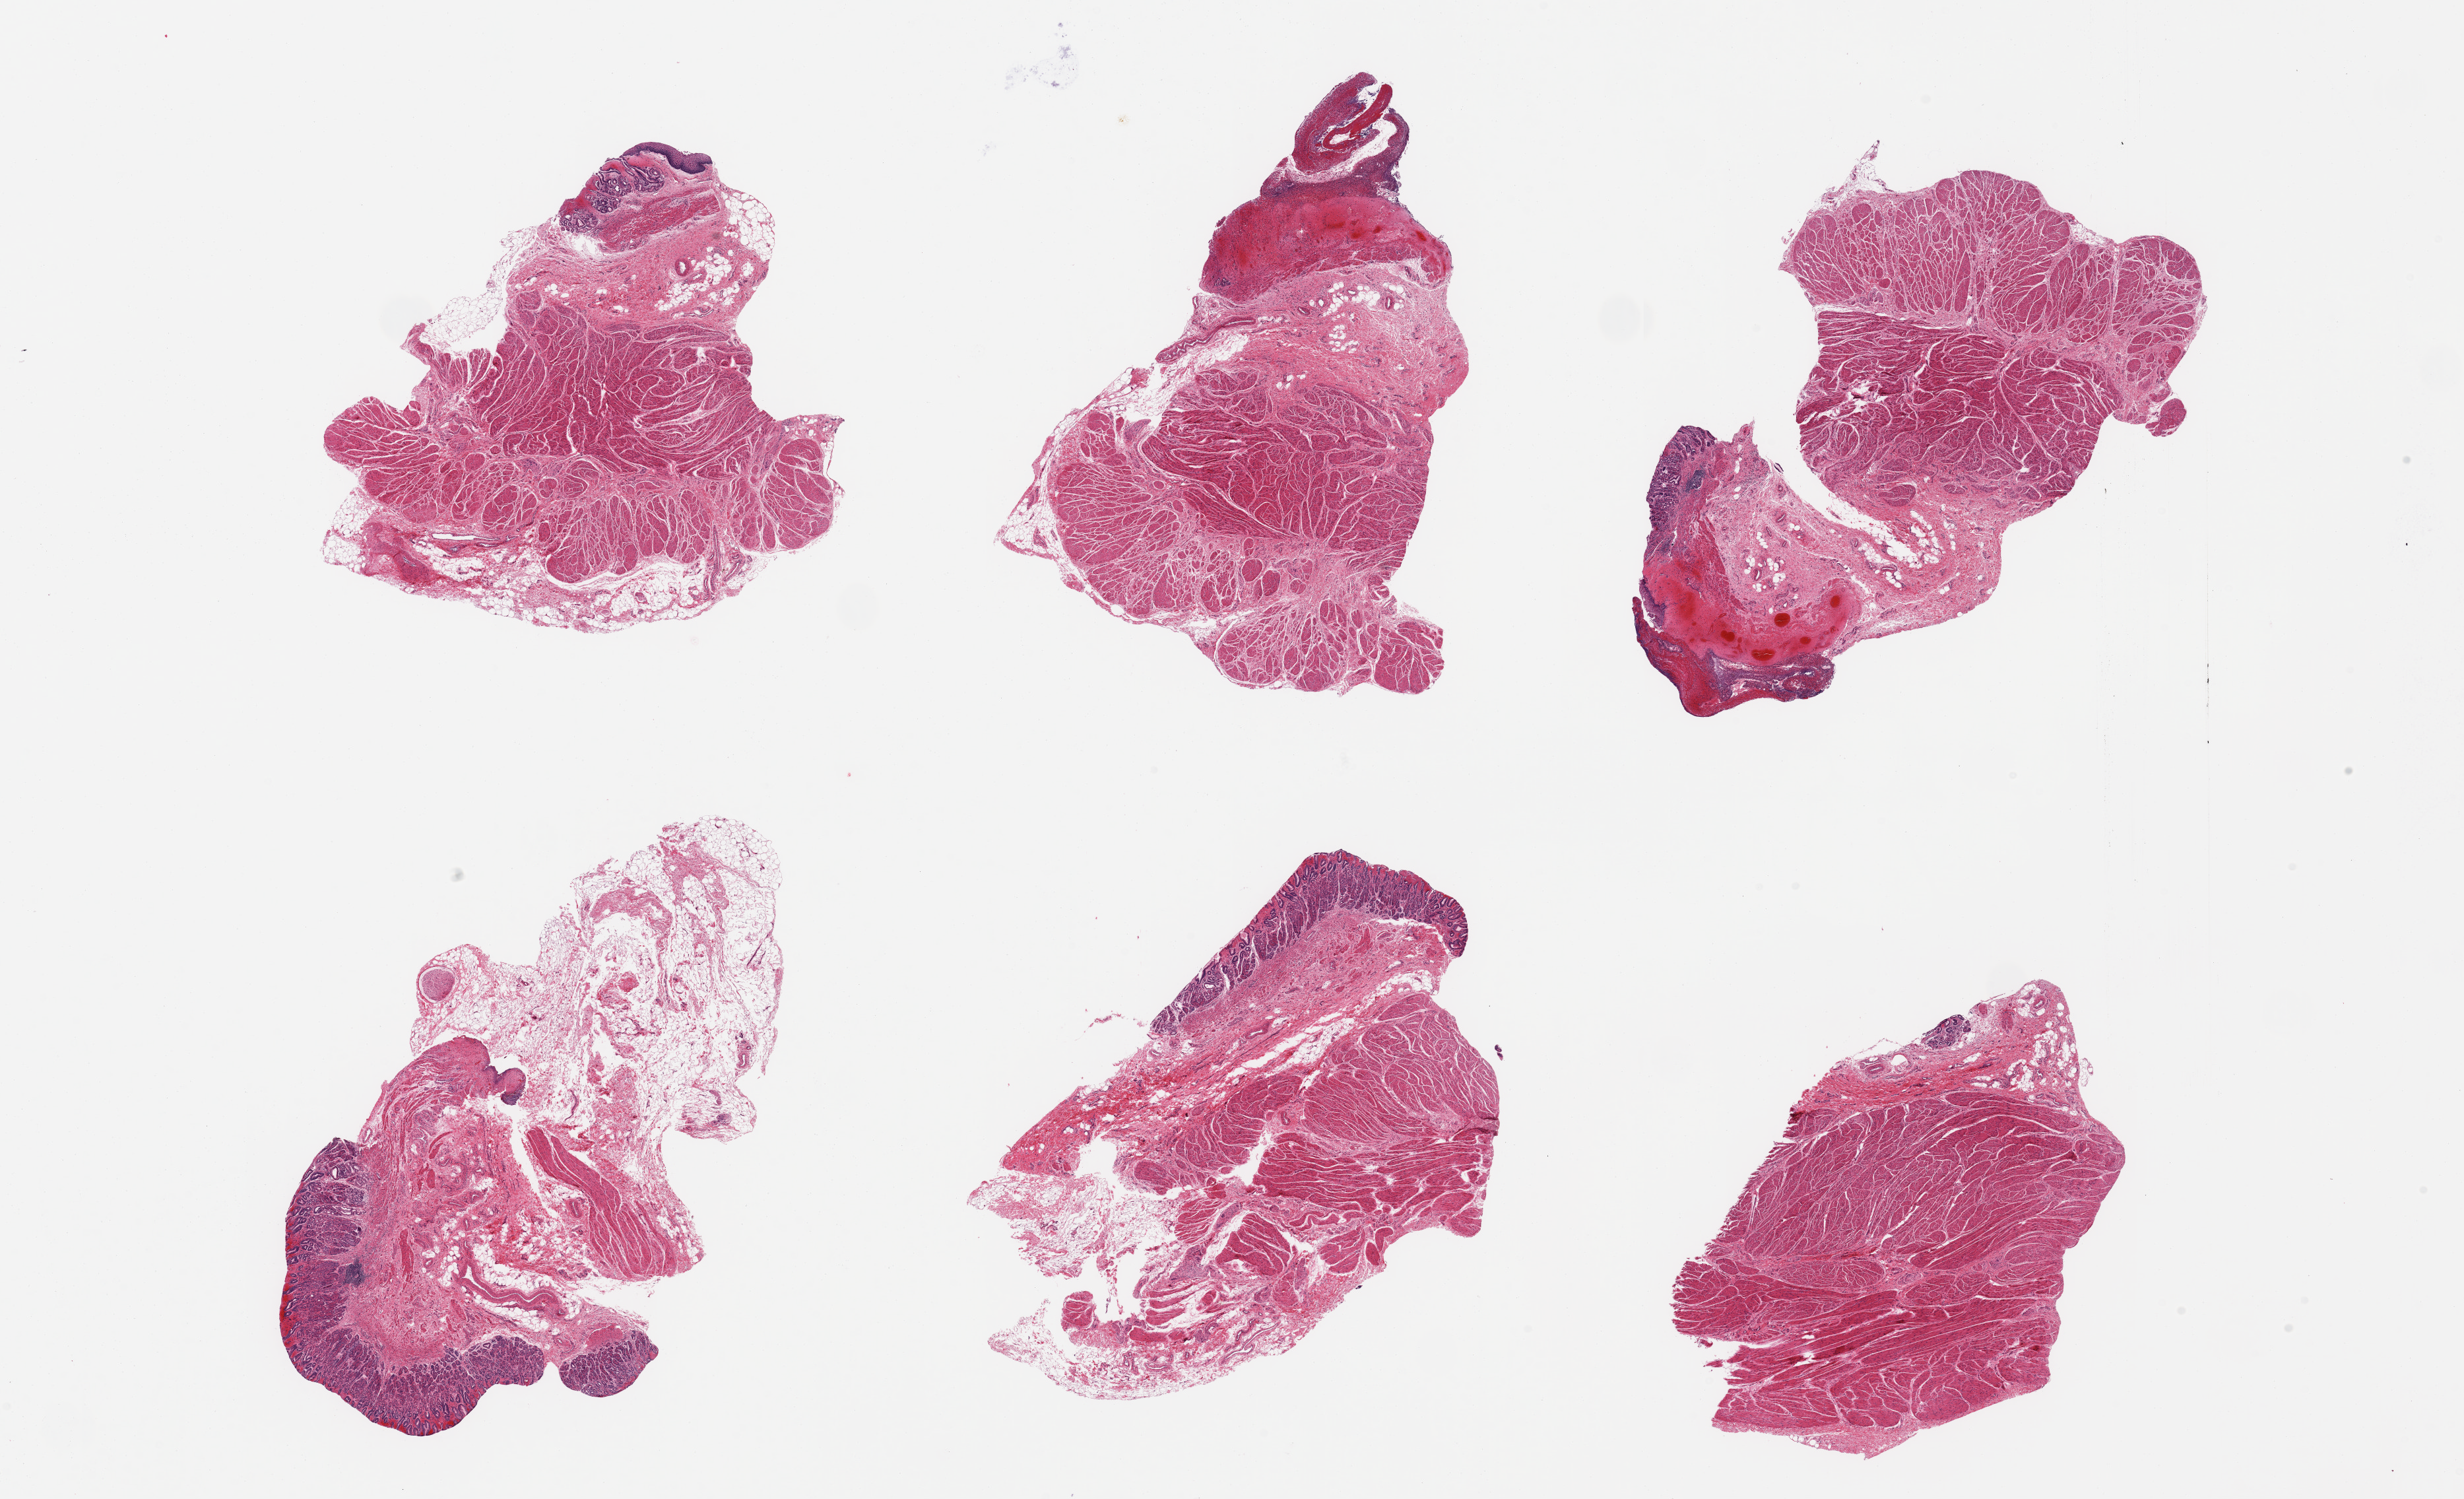
Haematoxylin and eosin whole-slide image — shown as a low-resolution overview of the whole scanned area (about 29.5 x 18.0 mm). PAXgene-fixed, paraffin-embedded tissue. Target tissue: gastroesophageal junction. Tissue donor sample. Donor sex: male.
Review note (as recorded): 6 pieces; muscularis with significant component of squamous and gastric mucosa with hemorrhage and ulcer.